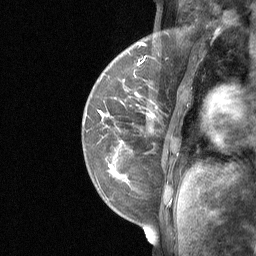
Breast MRI (dynamic contrast-enhanced), one sagittal slice. Position 15 of 64 along the scan axis. Dynamic contrast-enhanced study with each time point stored as its own series, time point 2 of 3 at this slice position (early post-contrast, ordered by acquisition time). 1.5 T. TE 4.8 ms, TR 27 ms. 256 × 256 image matrix, field of view 200 × 200 mm. Female patient, age 34 years. From the clinical record (not read from this slice): setting: breast cancer imaged before/during neoadjuvant chemotherapy; receptor status: HR-positive, HER2-negative.
Annotated regions visible in this slice (semi-automatically segmented with operator editing):
- analysis volume of interest (the breast-tissue region the enhancement analysis was run in; not a lesion): box from (x=92, y=50) to (x=188, y=185) px
- tumour enhancement mask (voxels above the 90 % enhancement threshold inside the analysis volume of interest): (x=98, y=62)–(x=140, y=168)